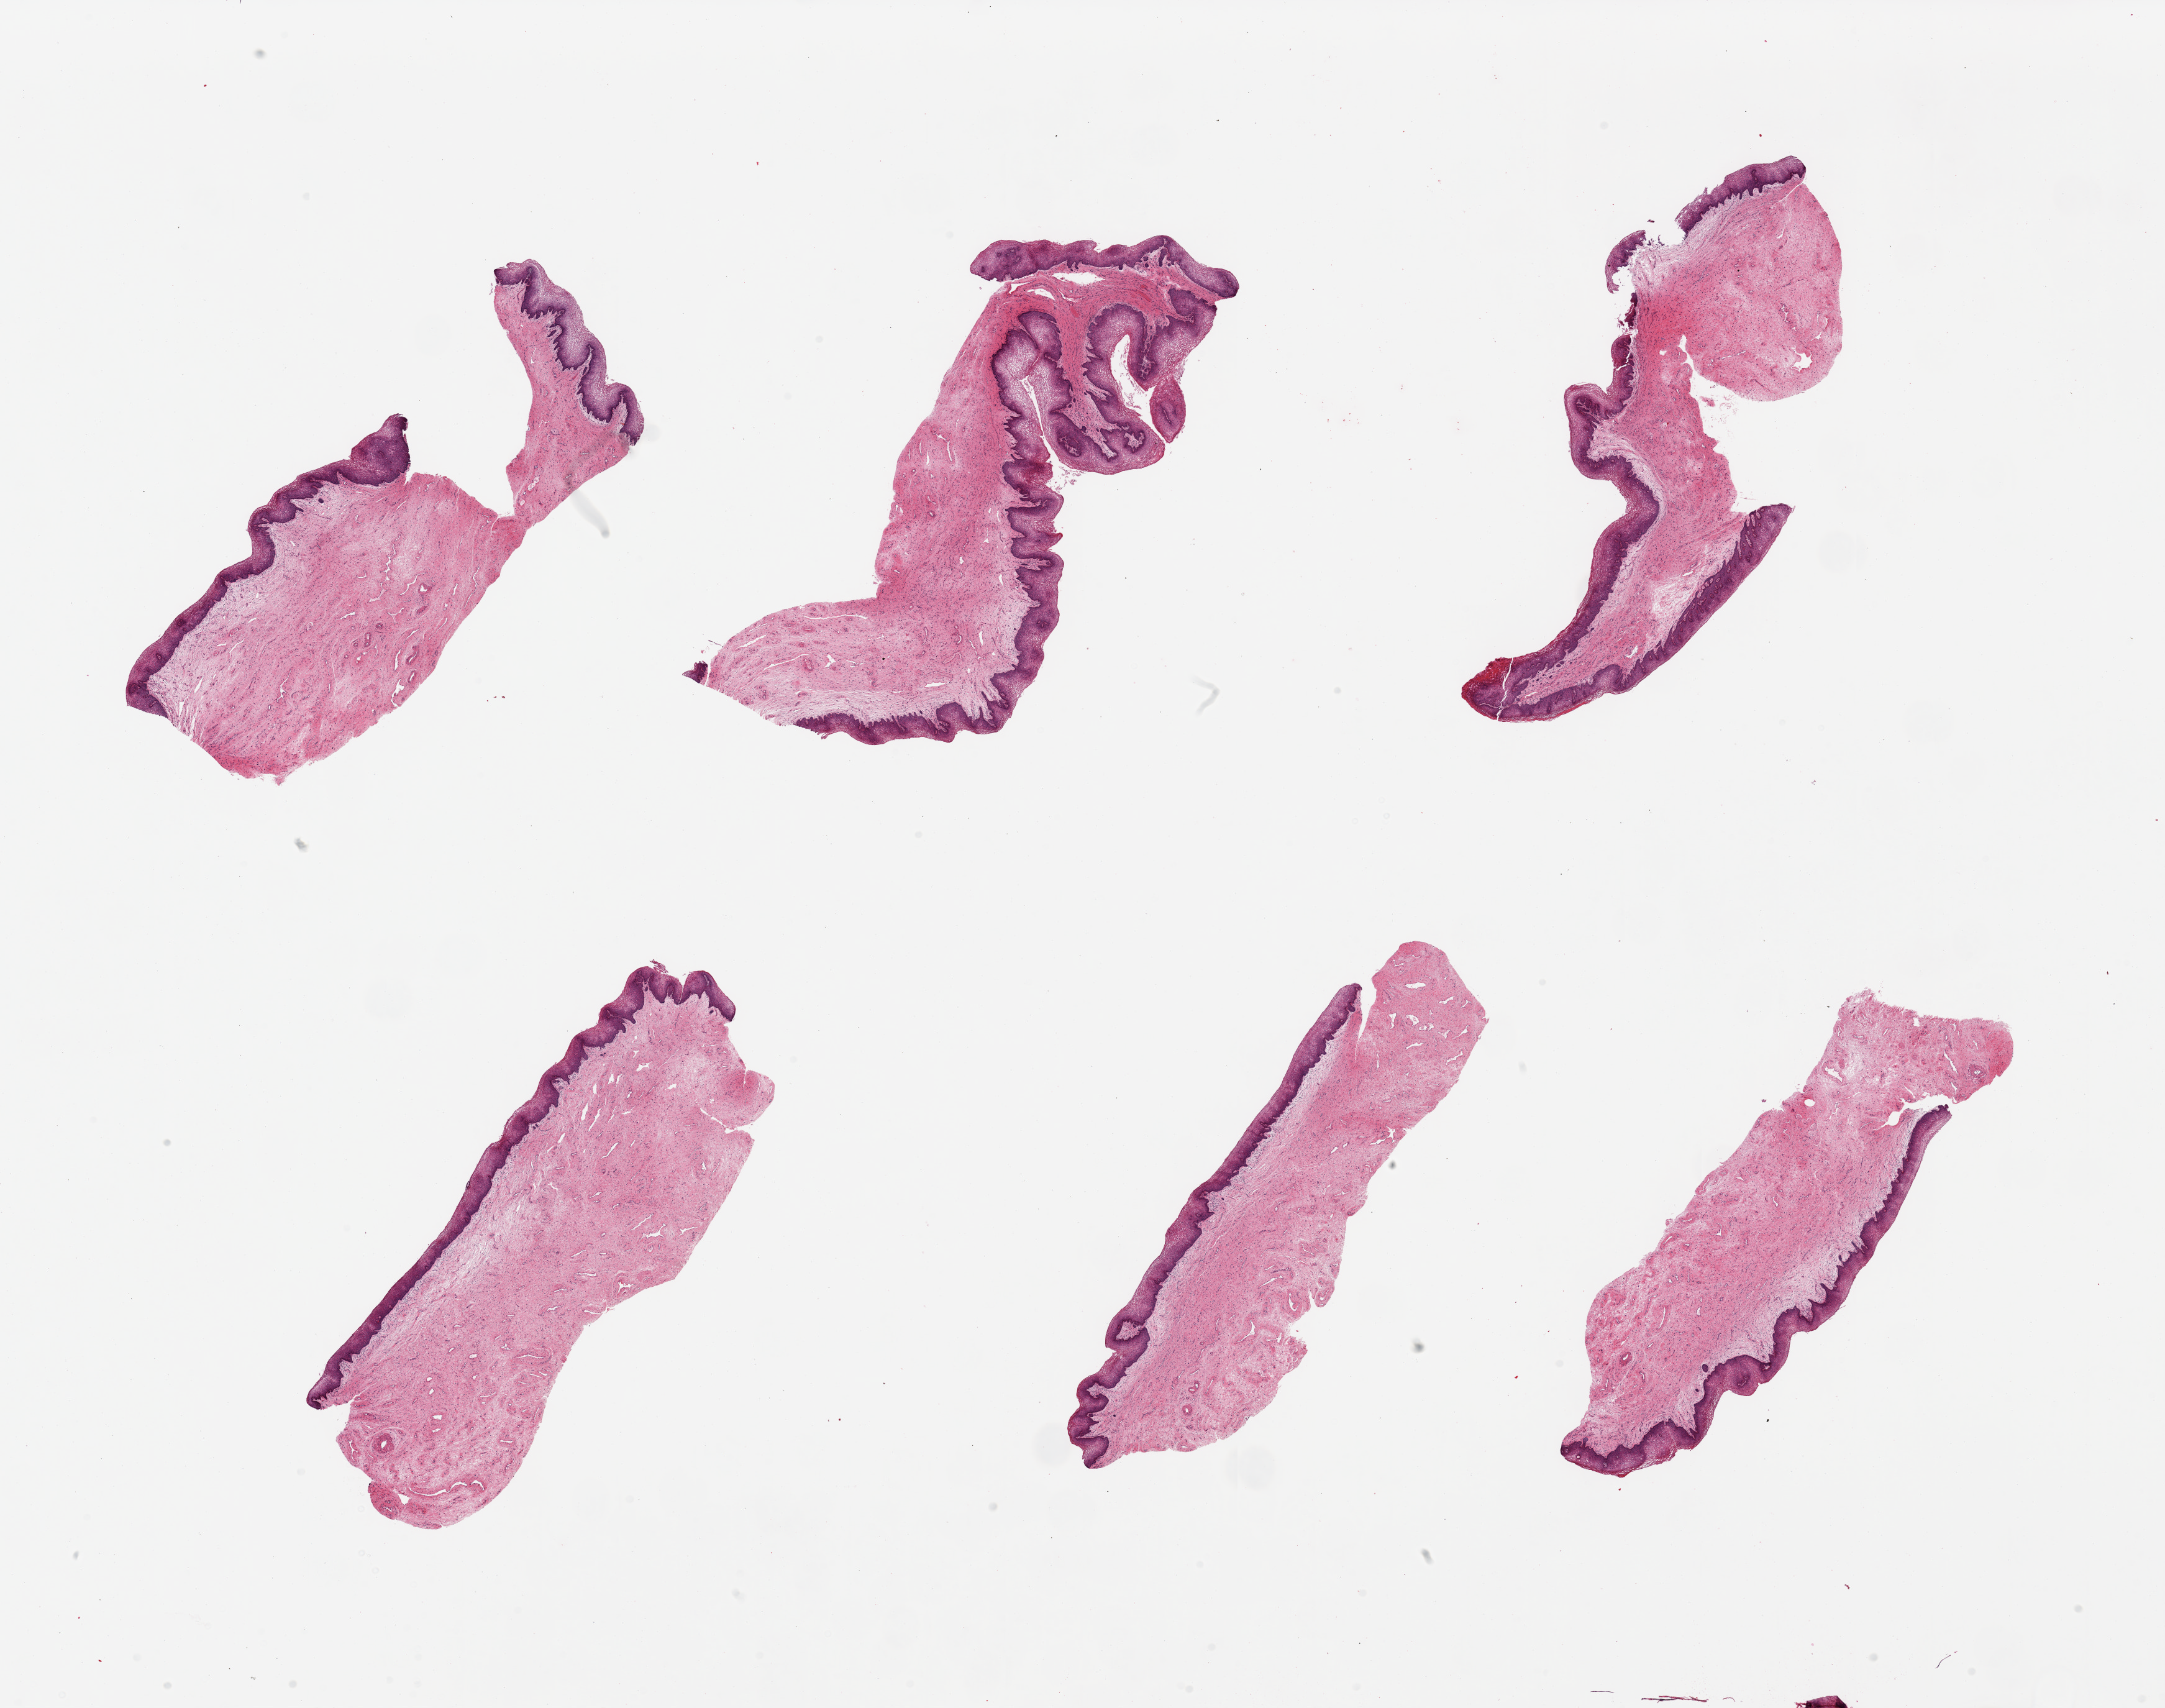
Whole-slide image, haematoxylin and eosin stain — a low-resolution overview of the entire scanned area, about 27.6 x 21.7 mm (slide scanned at 20x), PAXgene-fixed paraffin-embedded (PFPE) section, target tissue: vagina, tissue donor sample. Donor: female.
- reviewer comment on this tissue sample: 6 pieces